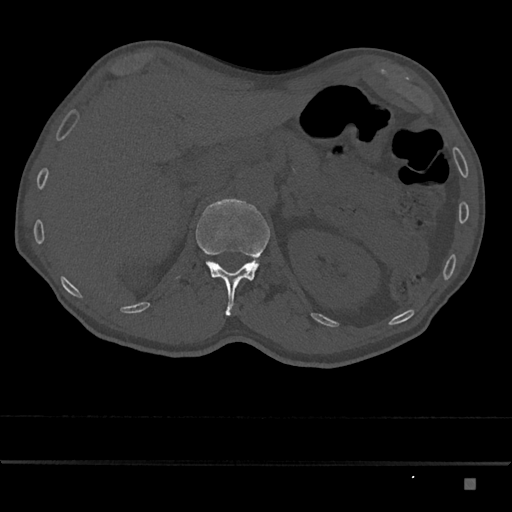
CT including the spine, one axial slice. Slice 542 of 797 in the series (ordered by position). Reconstruction kernel Br40s/3. 120 kVp. Bone window (W 1800 / L 400 HU). 512 × 512 image matrix, field of view 390 × 390 mm. Male patient, age 72 years. Case-level facts recorded for this patient, not image findings: primary cancer: prostate.
Annotated regions visible in this slice (semi-automatic segmentation, software-assisted and operator-edited):
- L1 vertebra: bounding box <196,198,270,316> (left, top, right, bottom; pixels)